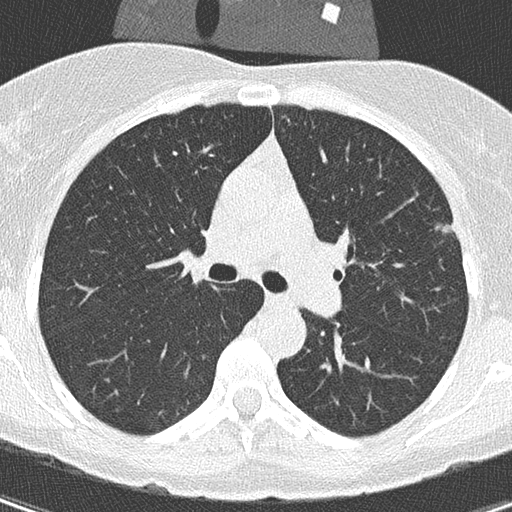
Axial slice from a low-dose chest CT screening exam, first (baseline) screen, lung window (W 1500 / L -600 HU), 2 mm slice thickness, 120 kVp, 512 × 512 image matrix, field of view 270 × 270 mm. Female participant, aged 56 years at enrolment. Former smoker at enrolment.
- Lesion marked by an expert reader, box from (x=421, y=191) to (x=472, y=243) px.
- The exam's reader record, not a measurement of the box and not confirmed to be the same lesion: non-calcified nodule or mass ≥4 mm, left upper lobe, 110 × 106 mm, spiculated (stellate) margins, soft tissue attenuation.
- Official screen result: positive, change unspecified: nodule(s) >= 4 mm or enlarging nodule(s), mass(es), or other non-specific abnormalities suspicious for lung cancer.
- Lung cancer was diagnosed 417 days after this screen: adenocarcinoma, NOS, left upper lobe, moderately differentiated (G2), stage IA (AJCC 6th edition), 11 mm at pathology.